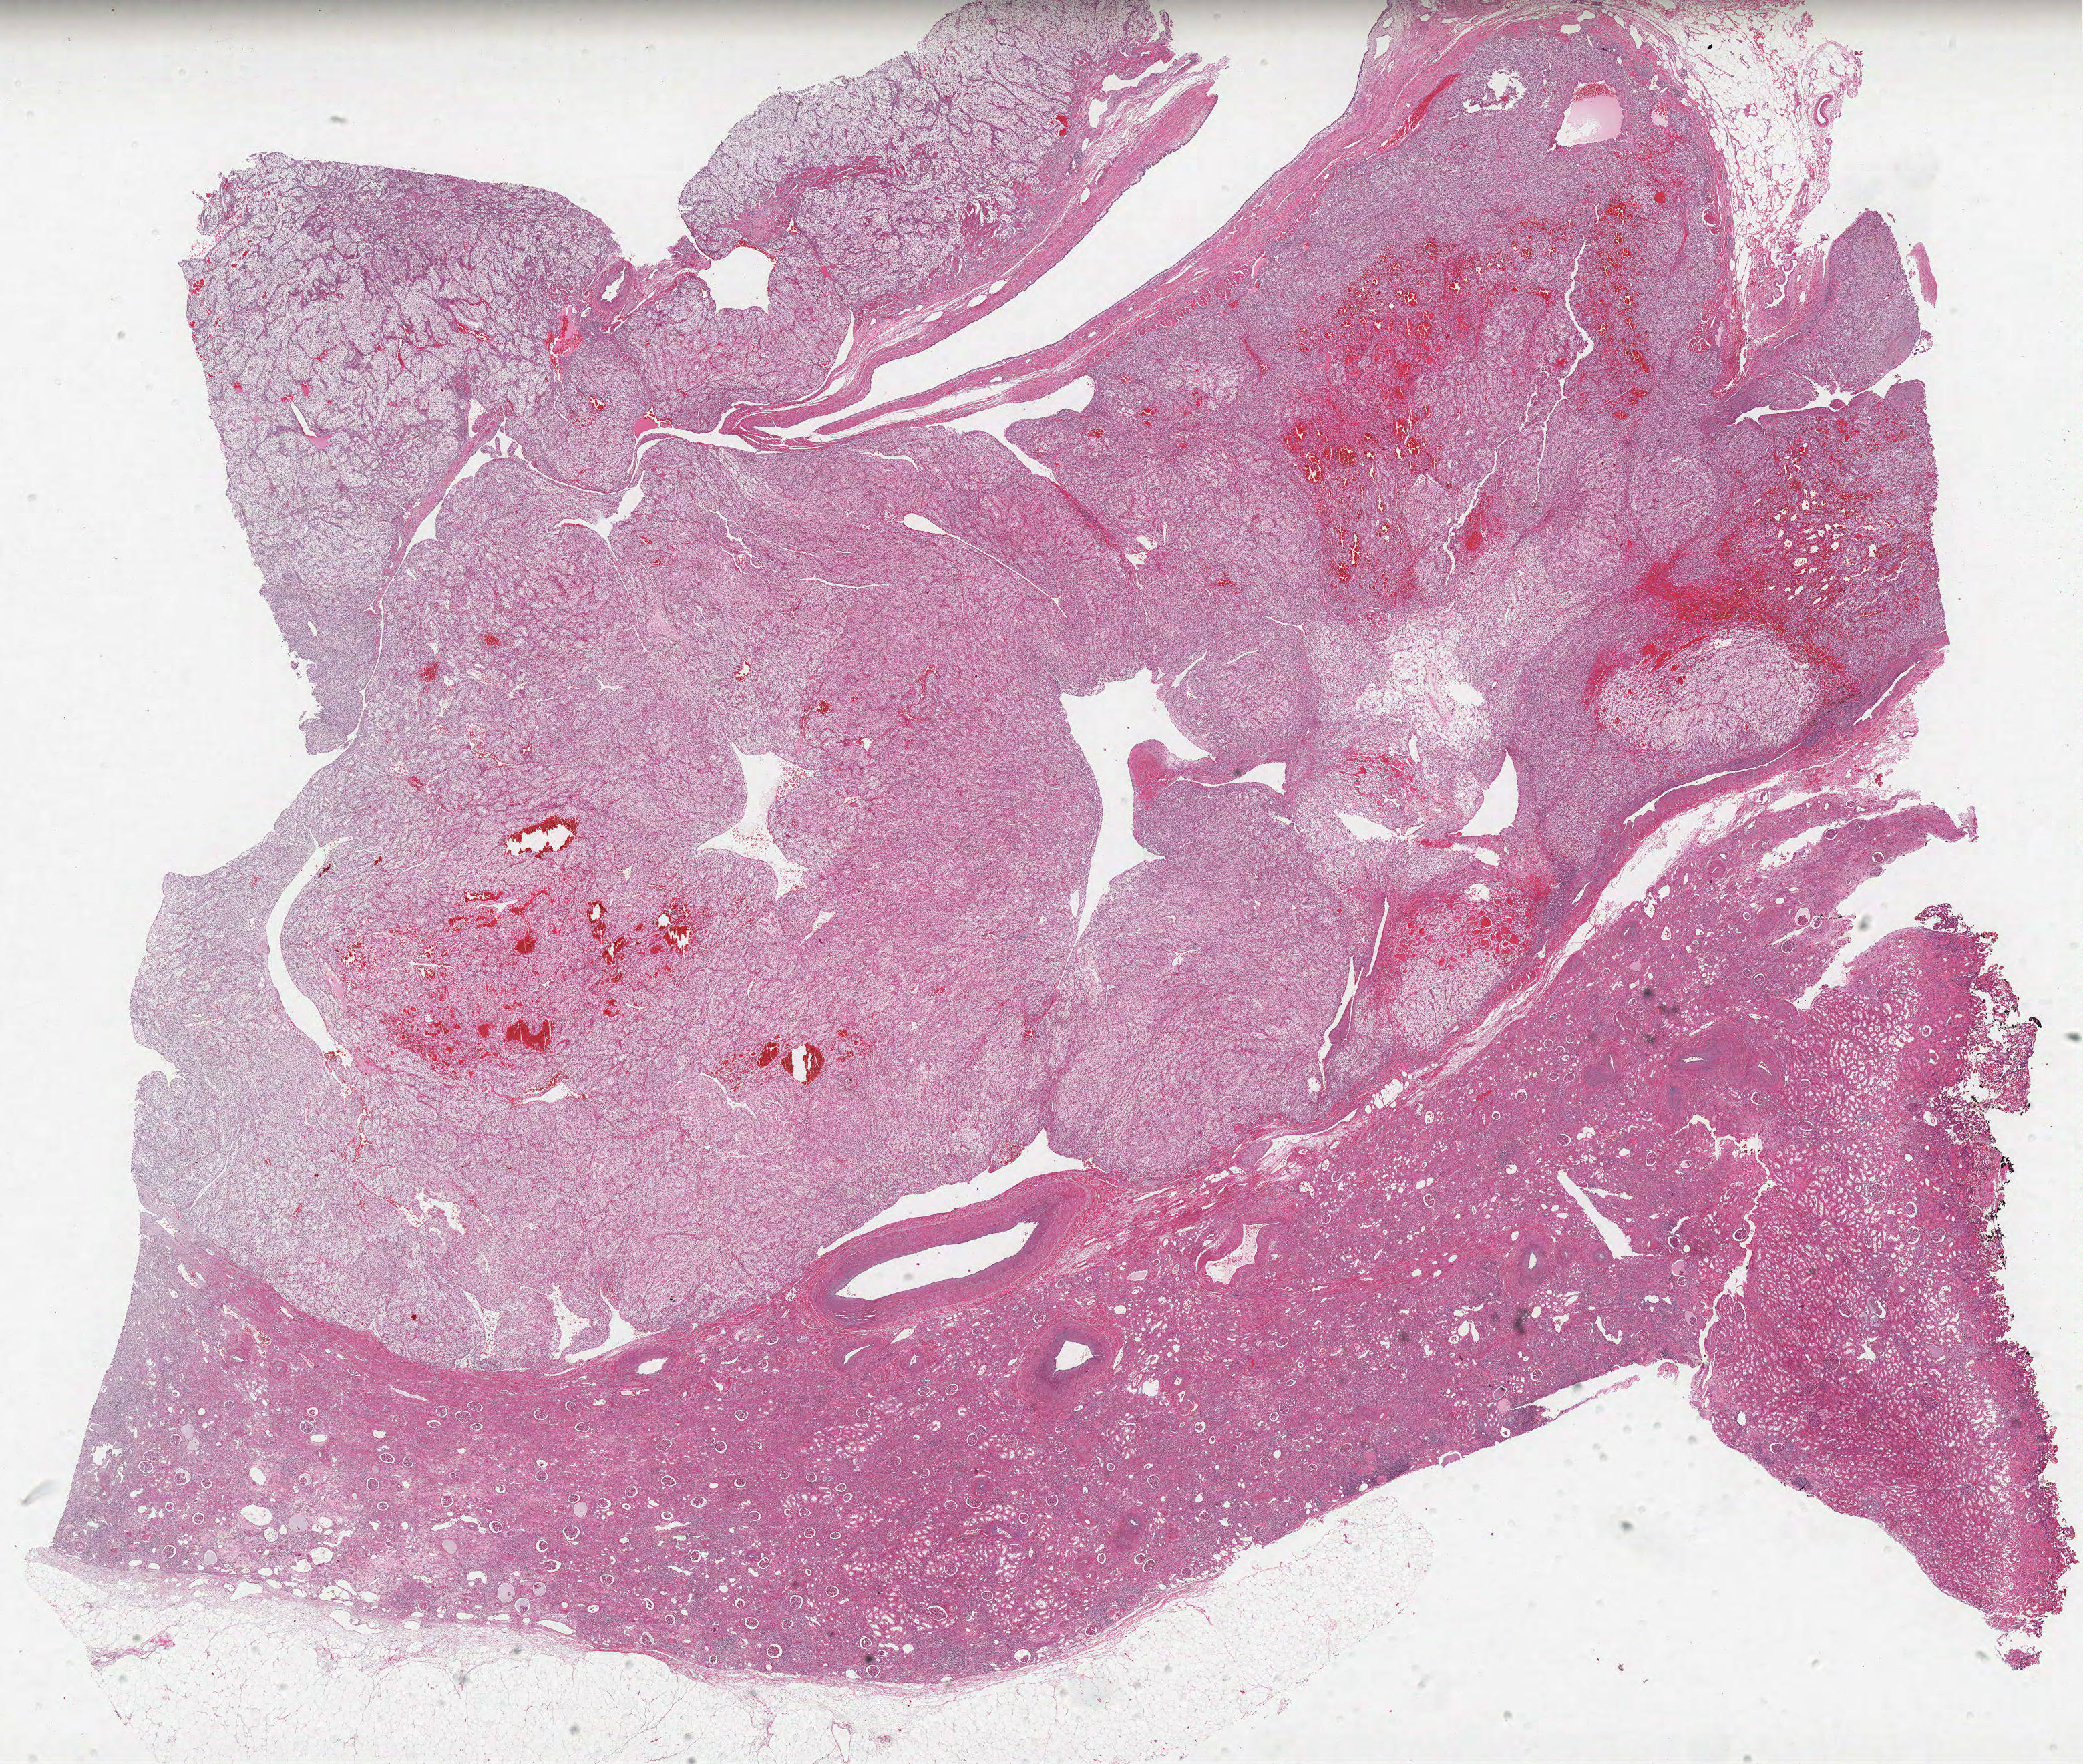
Whole-slide histology image, Hematoxylin and eosin (H&E) stained, whole scanned area (about 24.9 x 21.1 mm, slide scanned at 40x) shown as a low-resolution overview; FFPE section; sample: primary tumour, kidney. Male patient; age at initial diagnosis 72 years. Histologic grade: G3 (poorly differentiated).
Diagnosis: Clear cell adenocarcinoma, NOS. AJCC pathologic stage: III. Lymph nodes positive (case pathology): 0 of 9 examined. Laterality: right.